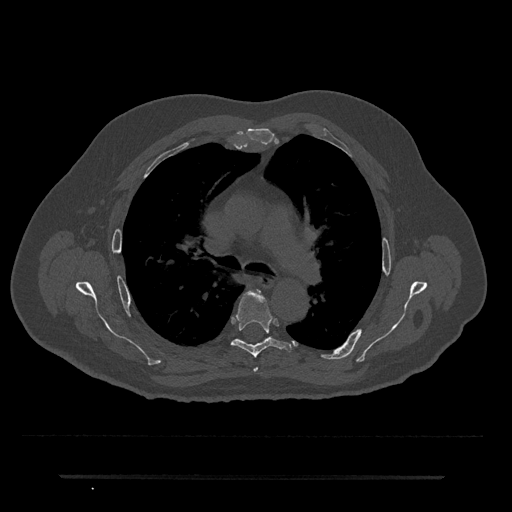
CT including the spine, one axial slice. Slice 484 of 797 in the series (ordered by position). 120 kVp. Bone window (W 1800 / L 400 HU). 512 × 512 image matrix, field of view 437 × 437 mm. Male patient, age 69 years. From the clinical record (not read from this slice): primary cancer: prostate.
Annotated regions visible in this slice (semi-automatic segmentation, software-assisted and operator-edited):
- T4 vertebra: bounding box (x1, y1, x2, y2) in pixels: (254, 368, 258, 372)
- T5 vertebra: (231, 290, 292, 358)